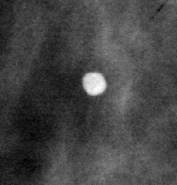
Cropped region of a digitized screen-film mammogram centred on a radiologist-marked abnormality; right breast; MLO view; BI-RADS breast density category 1 (scale 1–4).
Calcifications, morphology coarse; BI-RADS assessment category 2; benign without callback (not worked up further).